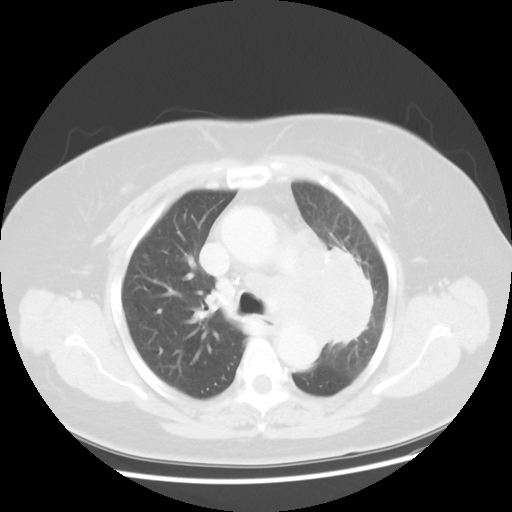
Chest CT, one axial slice. Position 32 of 49 along the scan axis. Lung window (W 1500 / L -600 HU). 5 mm slice thickness. 512 × 512 image matrix, field of view 374 × 374 mm. Patient: female, 58 years. Case-level facts recorded for this patient, not image findings: clinical TNM (as recorded): T4 N3 M0; histopathological grade: G3.
Structures marked on this image (rectangle marked by the reading radiologist):
- lung tumour (recorded histology: small cell carcinoma): bounding box [x1, y1, x2, y2] px = [274, 217, 376, 361]